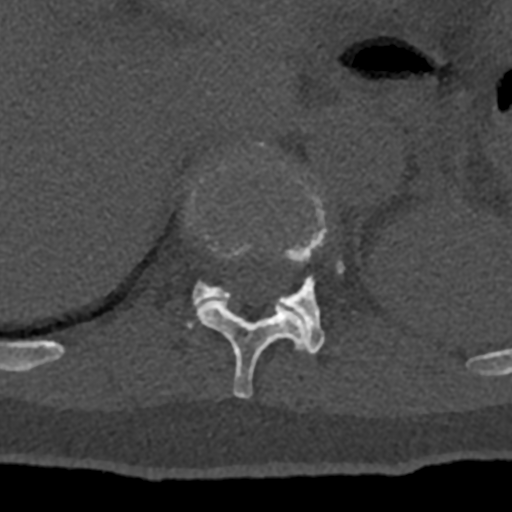
CT including the spine, one axial slice; slice 526 of 797 in the series (ordered by position); reconstruction kernel Br40s/3; bone window (W 1800 / L 400 HU); 0.5 mm slice thickness; 512 × 512 image matrix. Patient: male, 74 years. Case-level facts recorded for this patient, not image findings: primary cancer: renal.
Annotated regions visible in this slice (semi-automatic segmentation, software-assisted and operator-edited):
- T11 vertebra: bounding box <190,142,307,398> (left, top, right, bottom; pixels)
- T12 vertebra: <187,163,344,354>